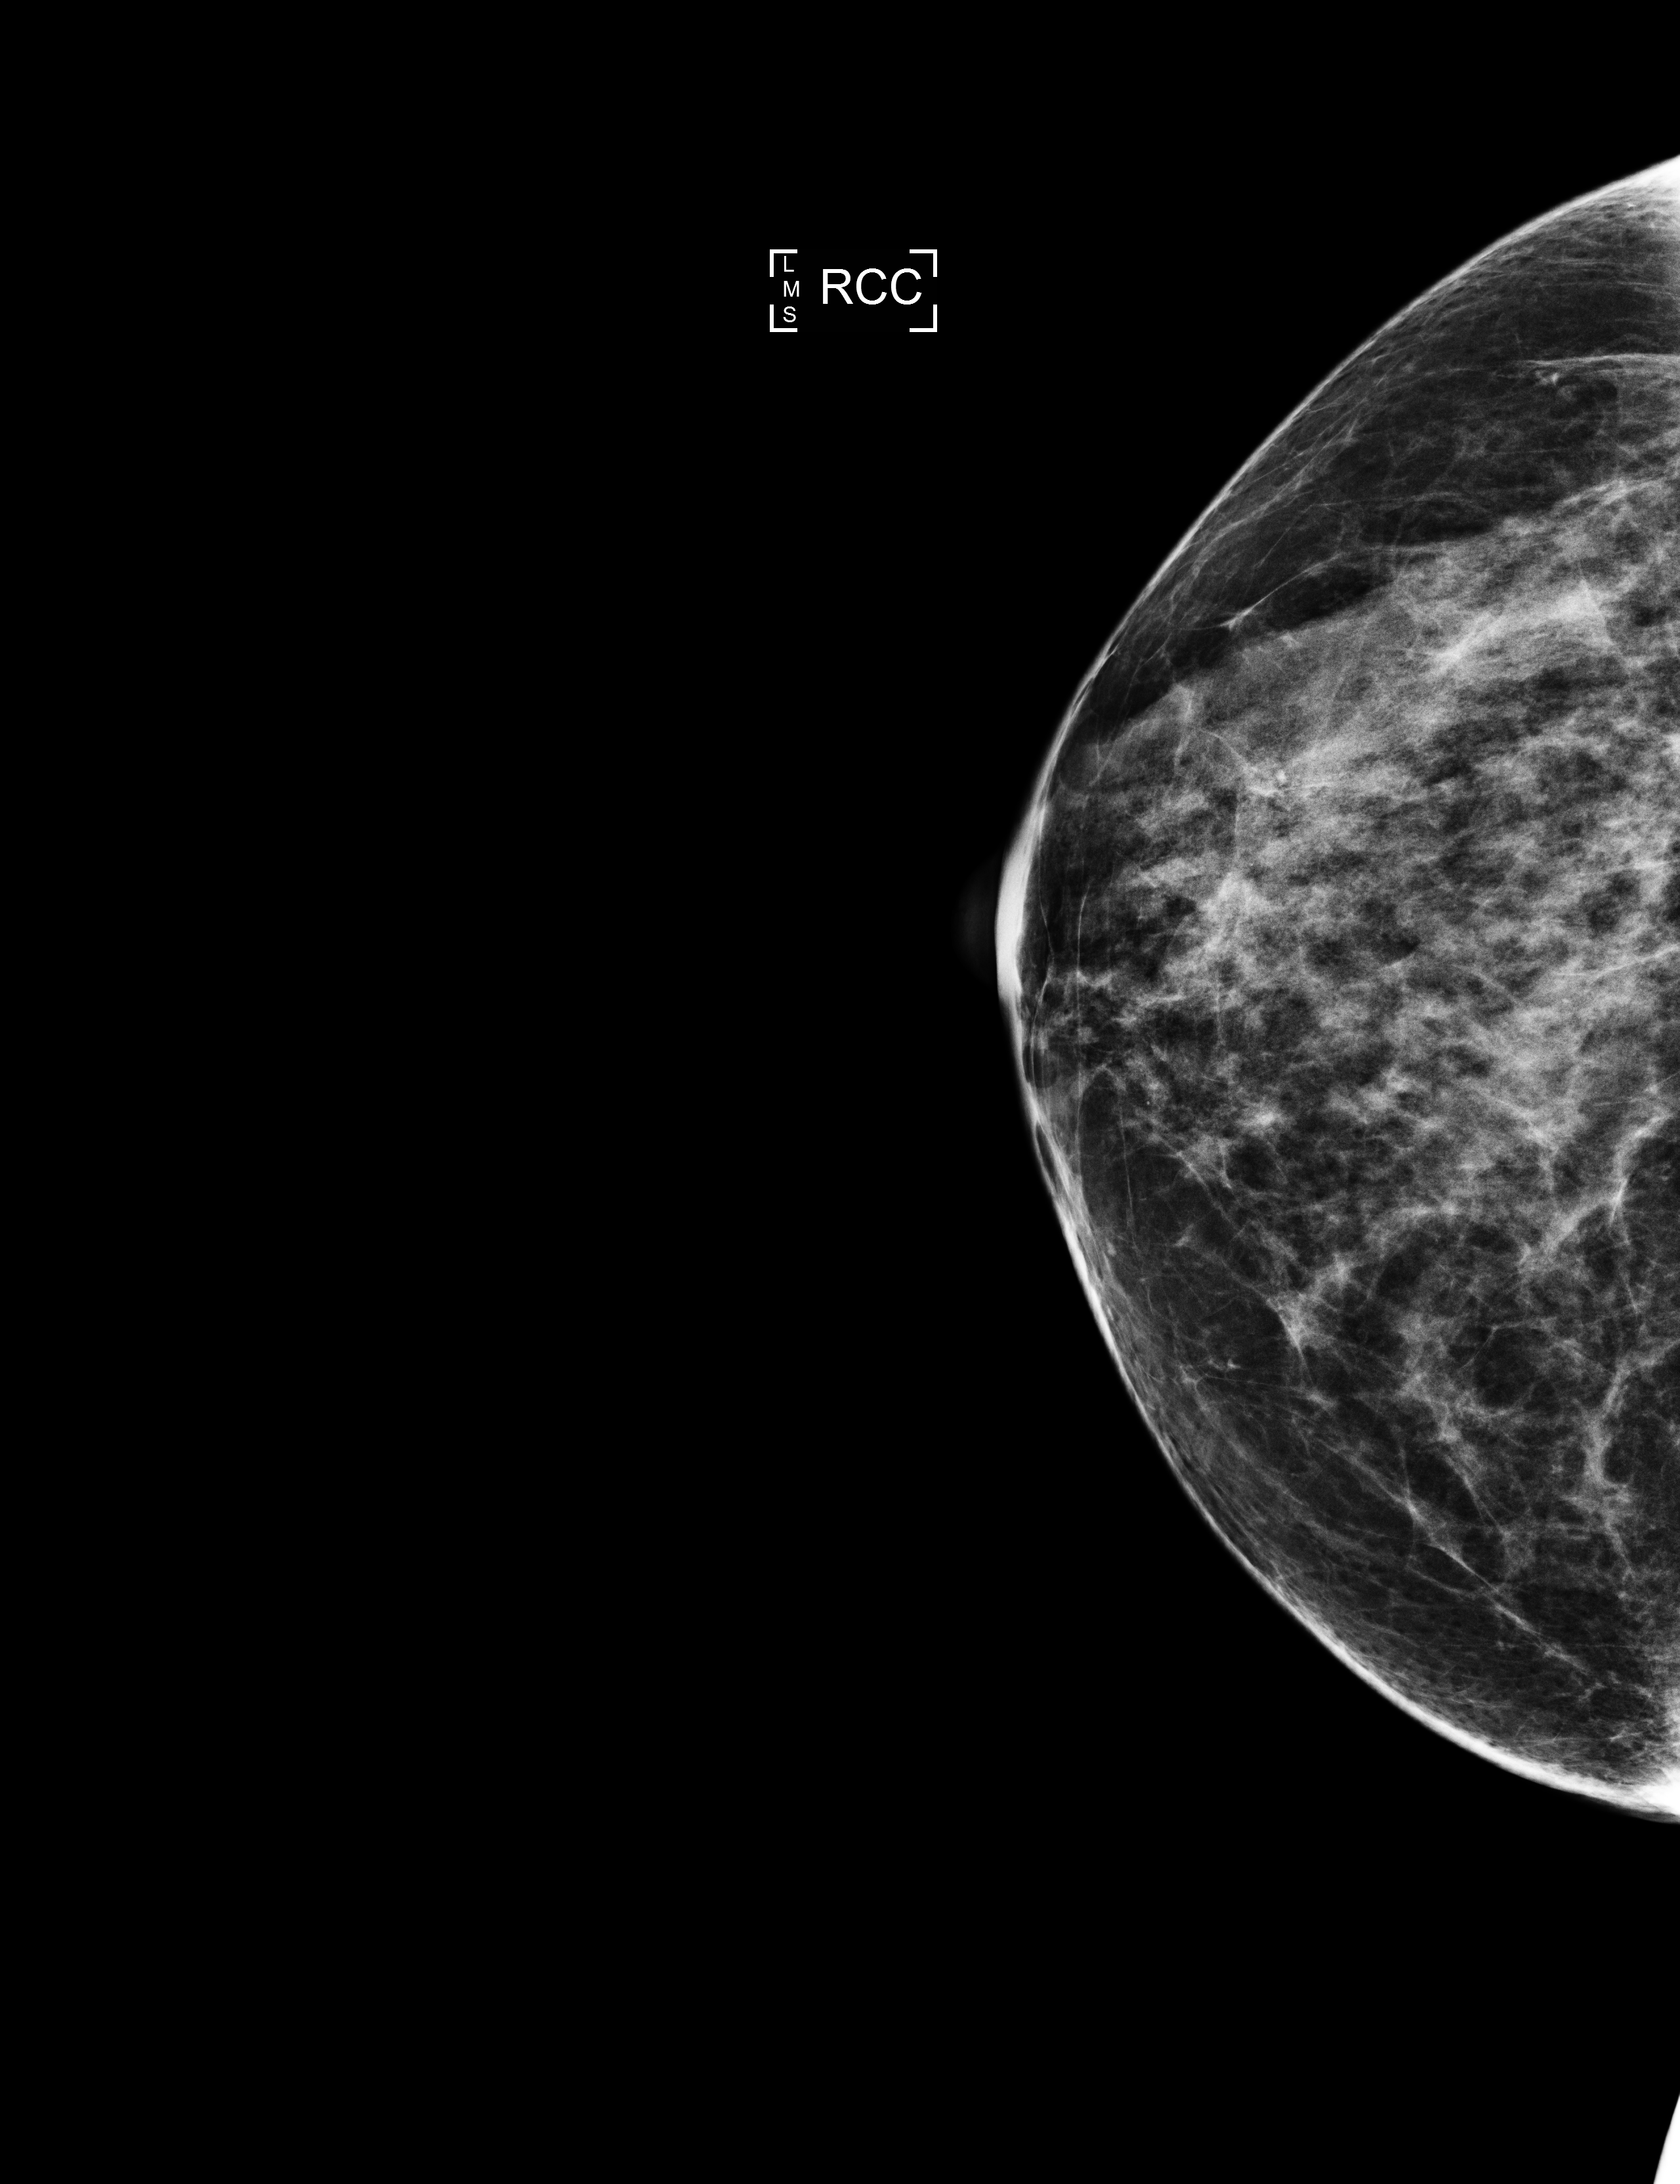
Screening examination, system: Selenia Dimensions. Patient aged 59 years (female).
Image type: full-field digital mammogram. Breast: right. Projection: CC view. Breast density at the screening exam (both breasts): heterogeneously dense (BI-RADS density category c). Final BI-RADS assessment for this screening round (tomosynthesis exam, both breasts): category 1. Recall: no recall after this screen.